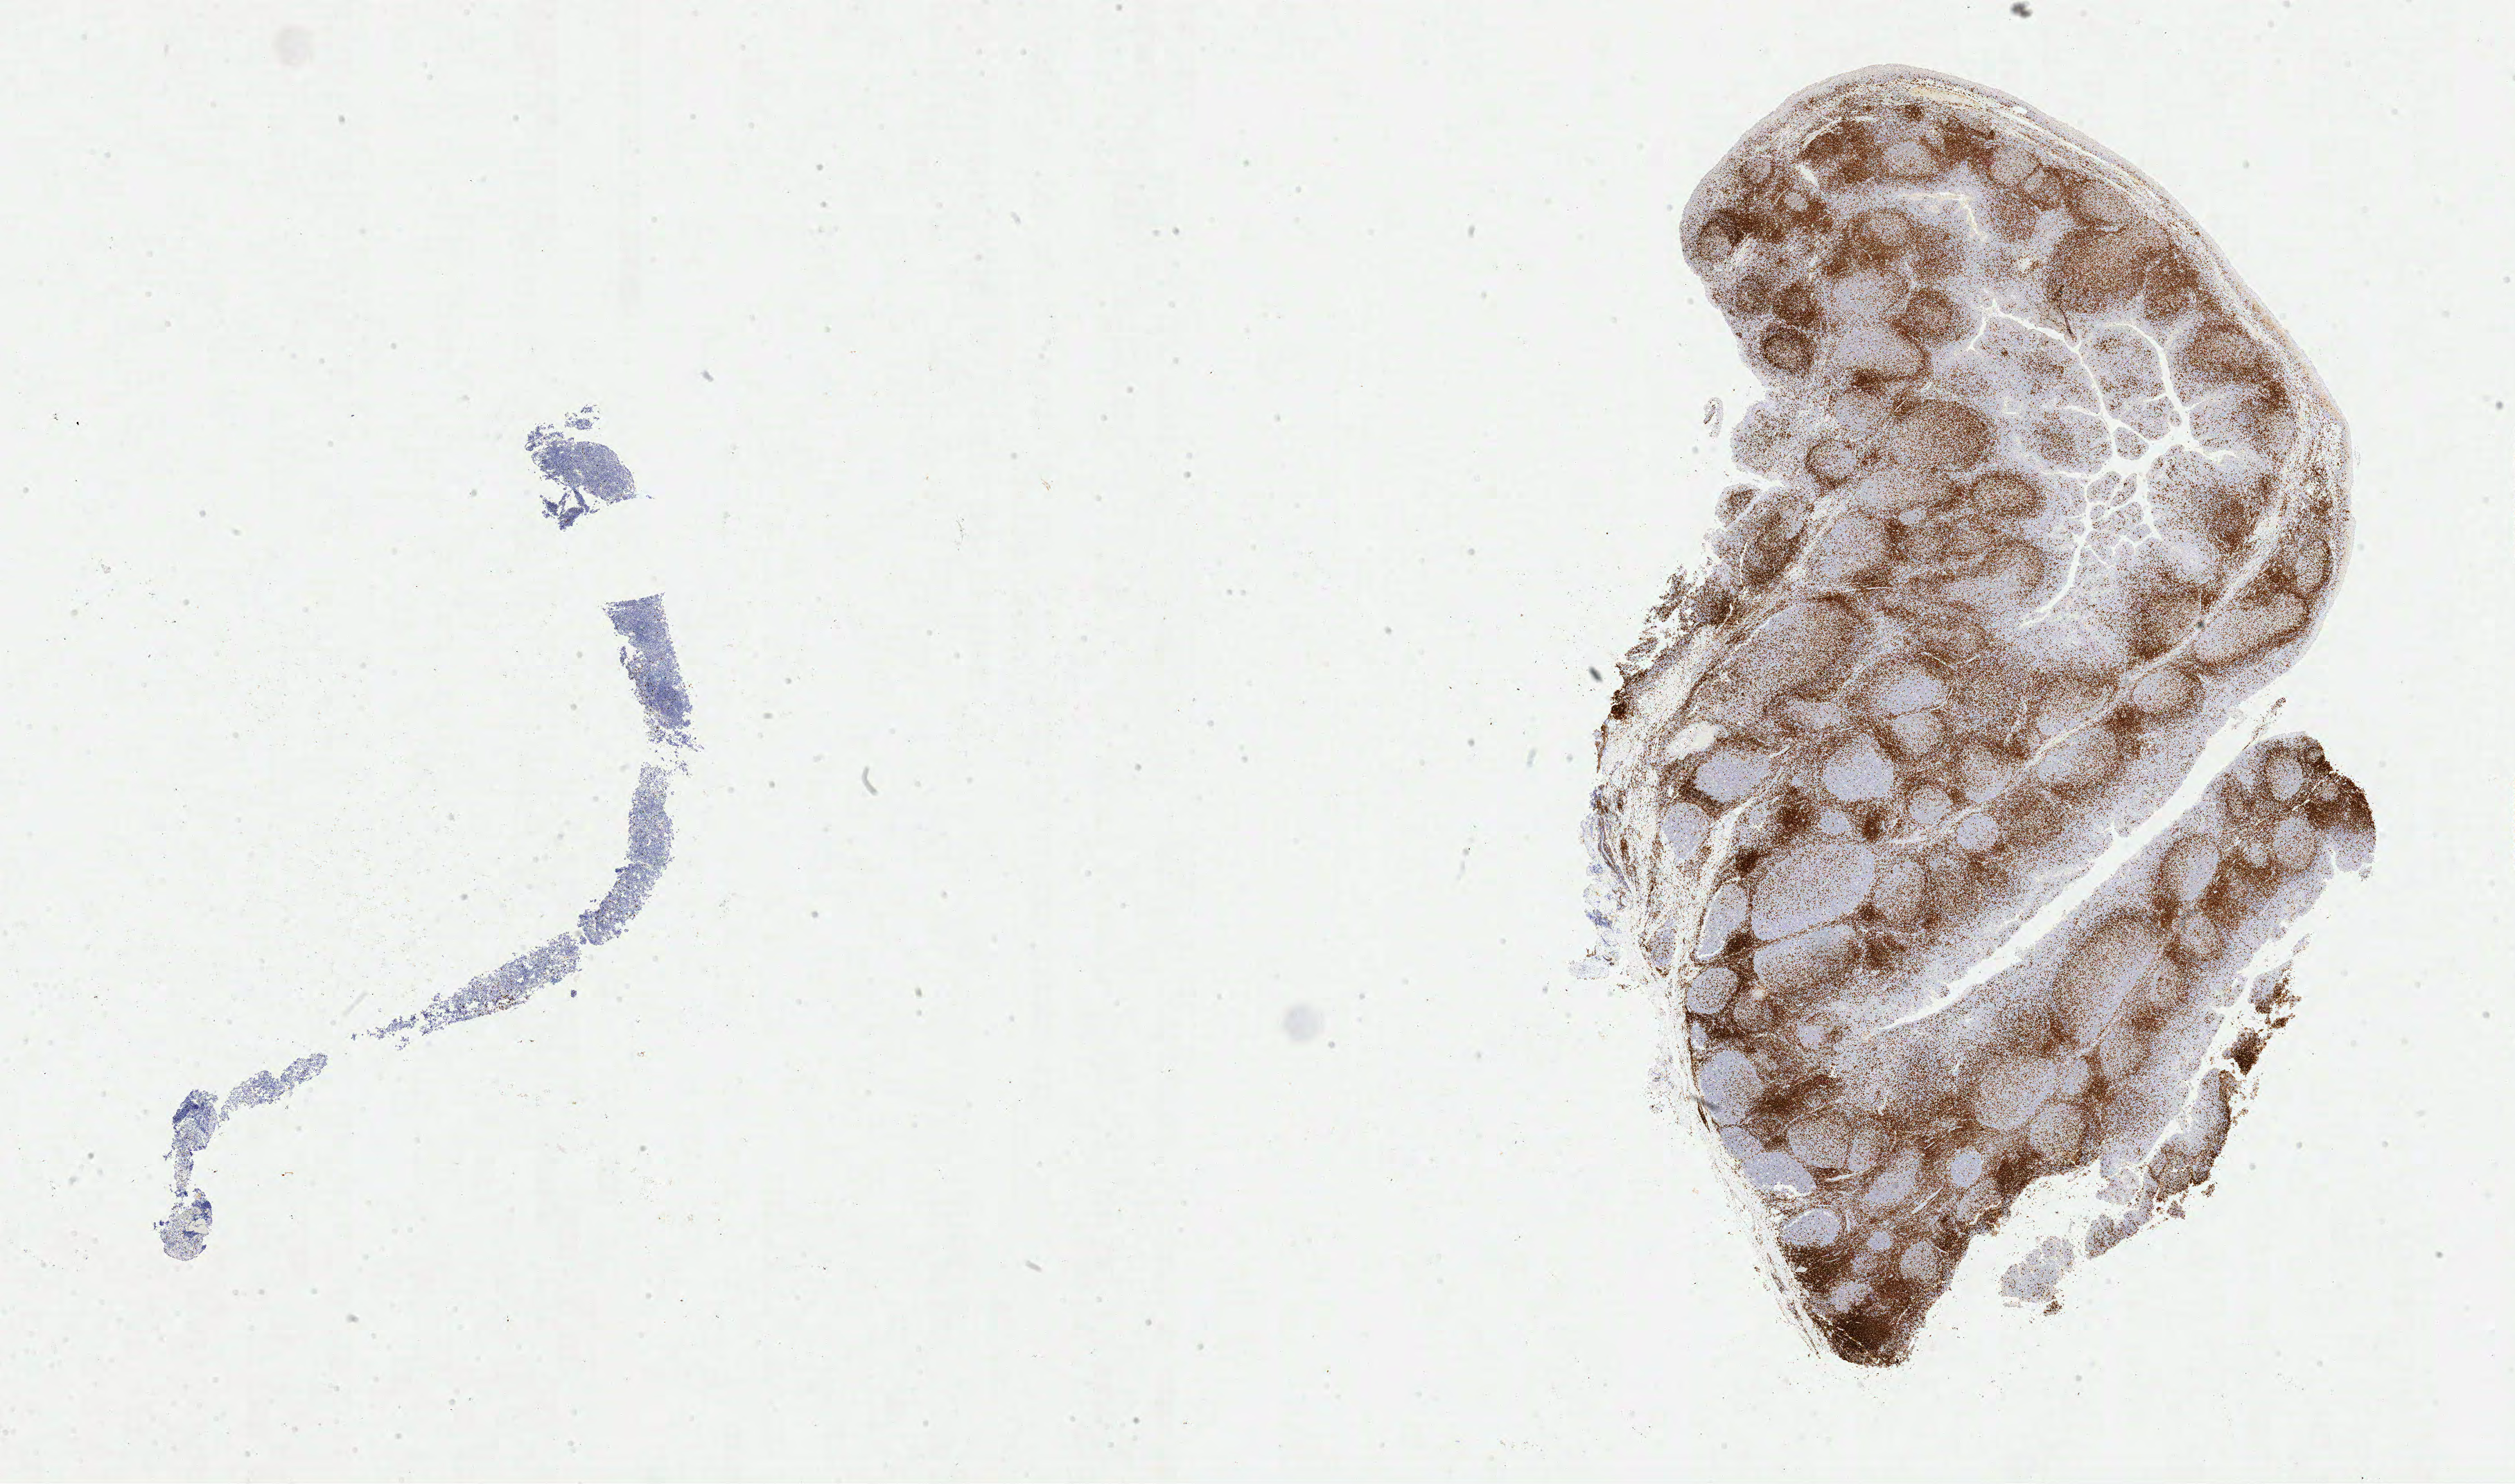
Immunohistochemistry (IHC) whole-slide image stained for CD3, whole scanned area (about 28.7 x 16.9 mm) shown as a low-resolution overview. Tumor tissue. Anatomic site: ovary. Patient: female, age at initial diagnosis 7 years.
Diagnosis: Burkitt lymphoma, NOS.